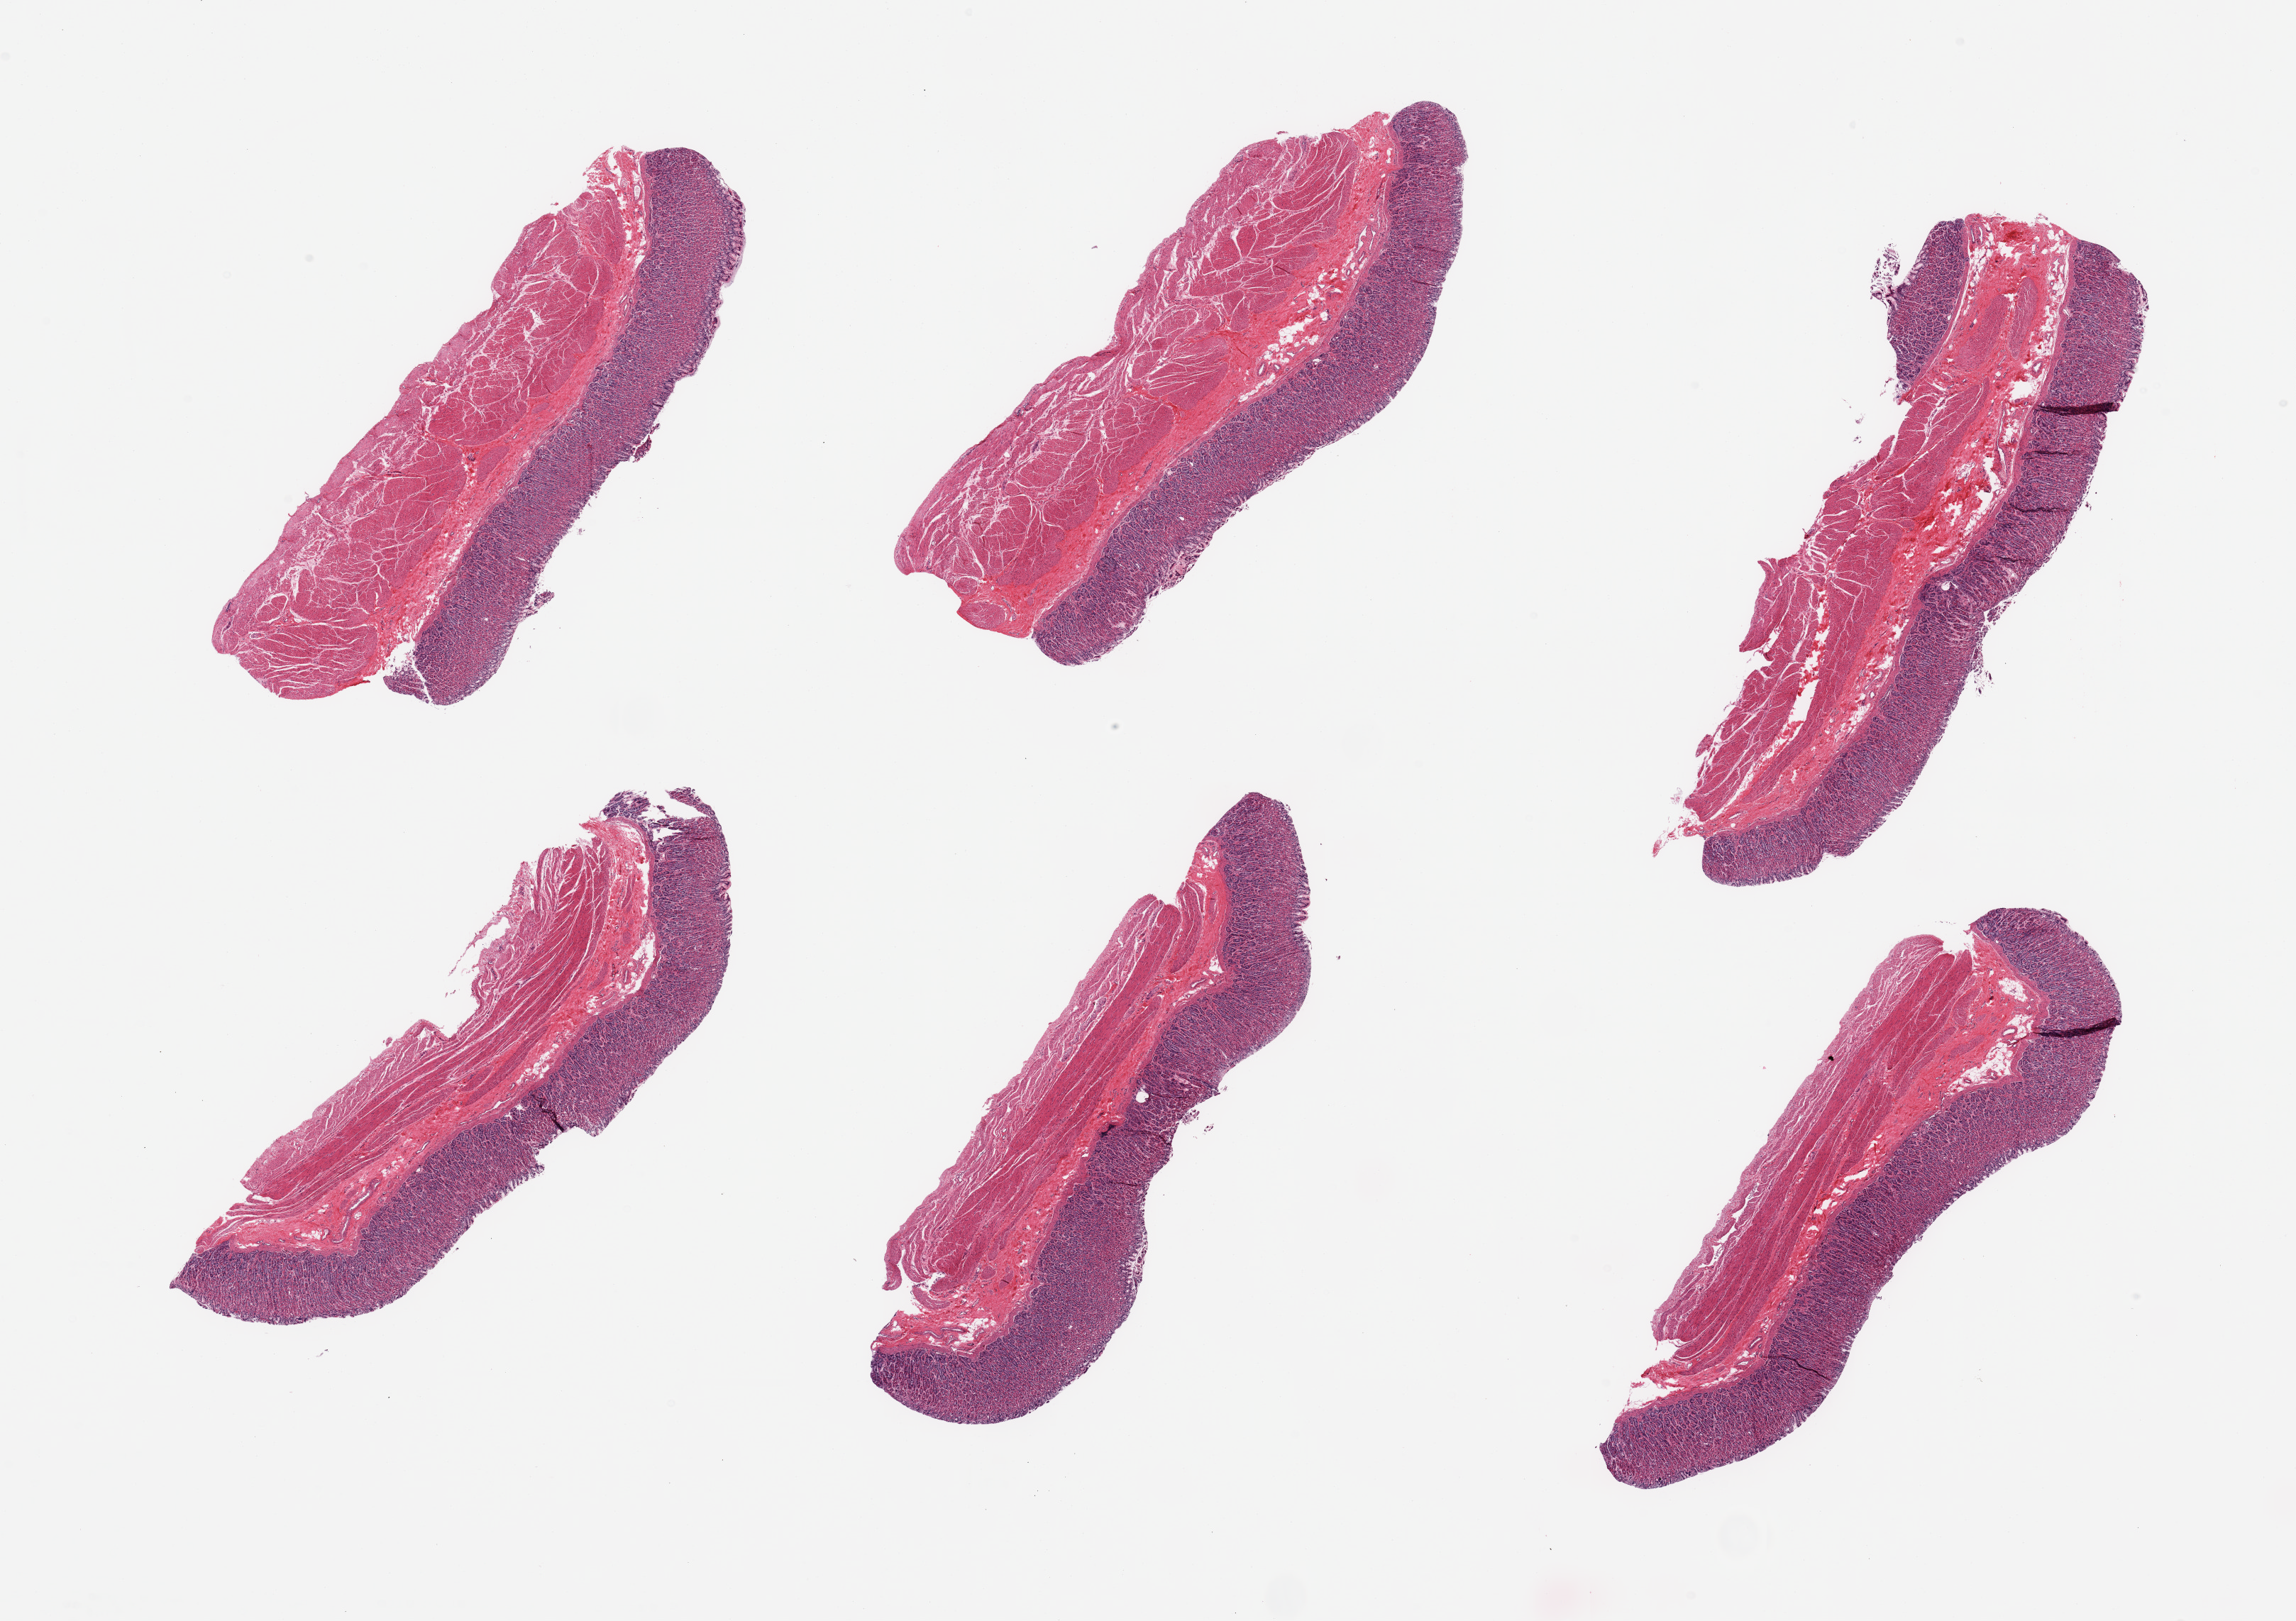
Hematoxylin and eosin (H&E) whole-slide image — low-resolution overview of the scanned area, about 25.6 x 18.1 mm (slide scanned at 20x). PAXgene-fixed paraffin-embedded (PFPE) section. Target tissue: stomach. Tissue donor sample.
* reviewer comment on this tissue sample: 6 pieces; superficial mucosal autolysis & sloughing